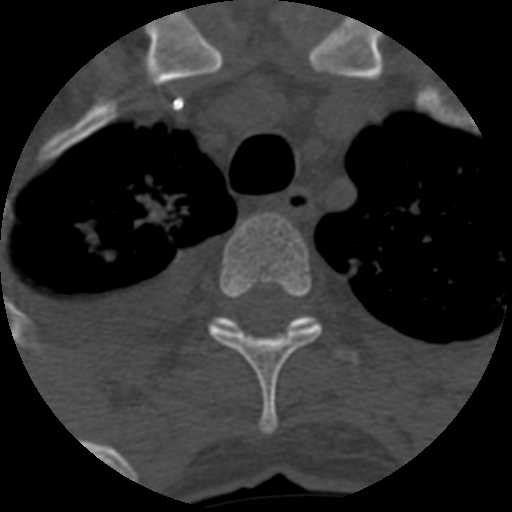
CT including the spine, one axial slice; position 485 of 708 along the scan axis; 120 kVp; one of 3 acquisitions stored at this slice position; bone window (W 1800 / L 400 HU); 1.25 mm slice thickness; 512 × 512 image matrix, field of view 160 × 160 mm. Patient age 55 years. Case-level facts recorded for this patient, not image findings: primary cancer: colon; vertebrae with lytic lesions (as recorded): T12, L1, L5.
Structures marked on this image (semi-automatic segmentation, software-assisted and operator-edited):
- T3 vertebra: bounding box [x1, y1, x2, y2] px = [208, 213, 322, 434]
- T4 vertebra: [213, 316, 359, 365]